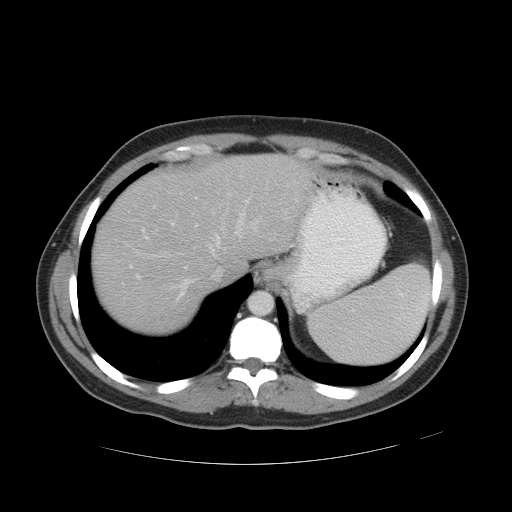
Contrast-enhanced abdominal CT, one axial slice; position 41 of 49 along the scan axis; 120 kVp; intravenous contrast given; soft-tissue window (W 400 / L 40 HU); 5 mm slice thickness; 512 × 512 image matrix. Male patient, age 42 years. From the clinical record (not read from this slice): diagnosis: colorectal cancer liver metastases, imaged before liver resection; multiple liver metastases: yes.
Structures marked on this image (expert manual segmentation):
- hepatic veins: bounding box [x1, y1, x2, y2] px = [145, 193, 260, 303]
- liver: [93, 156, 308, 333]
- planned liver remnant (the part of the liver to remain after resection): [93, 156, 308, 333]
- portal vein (with intrahepatic branches): [129, 175, 268, 279]